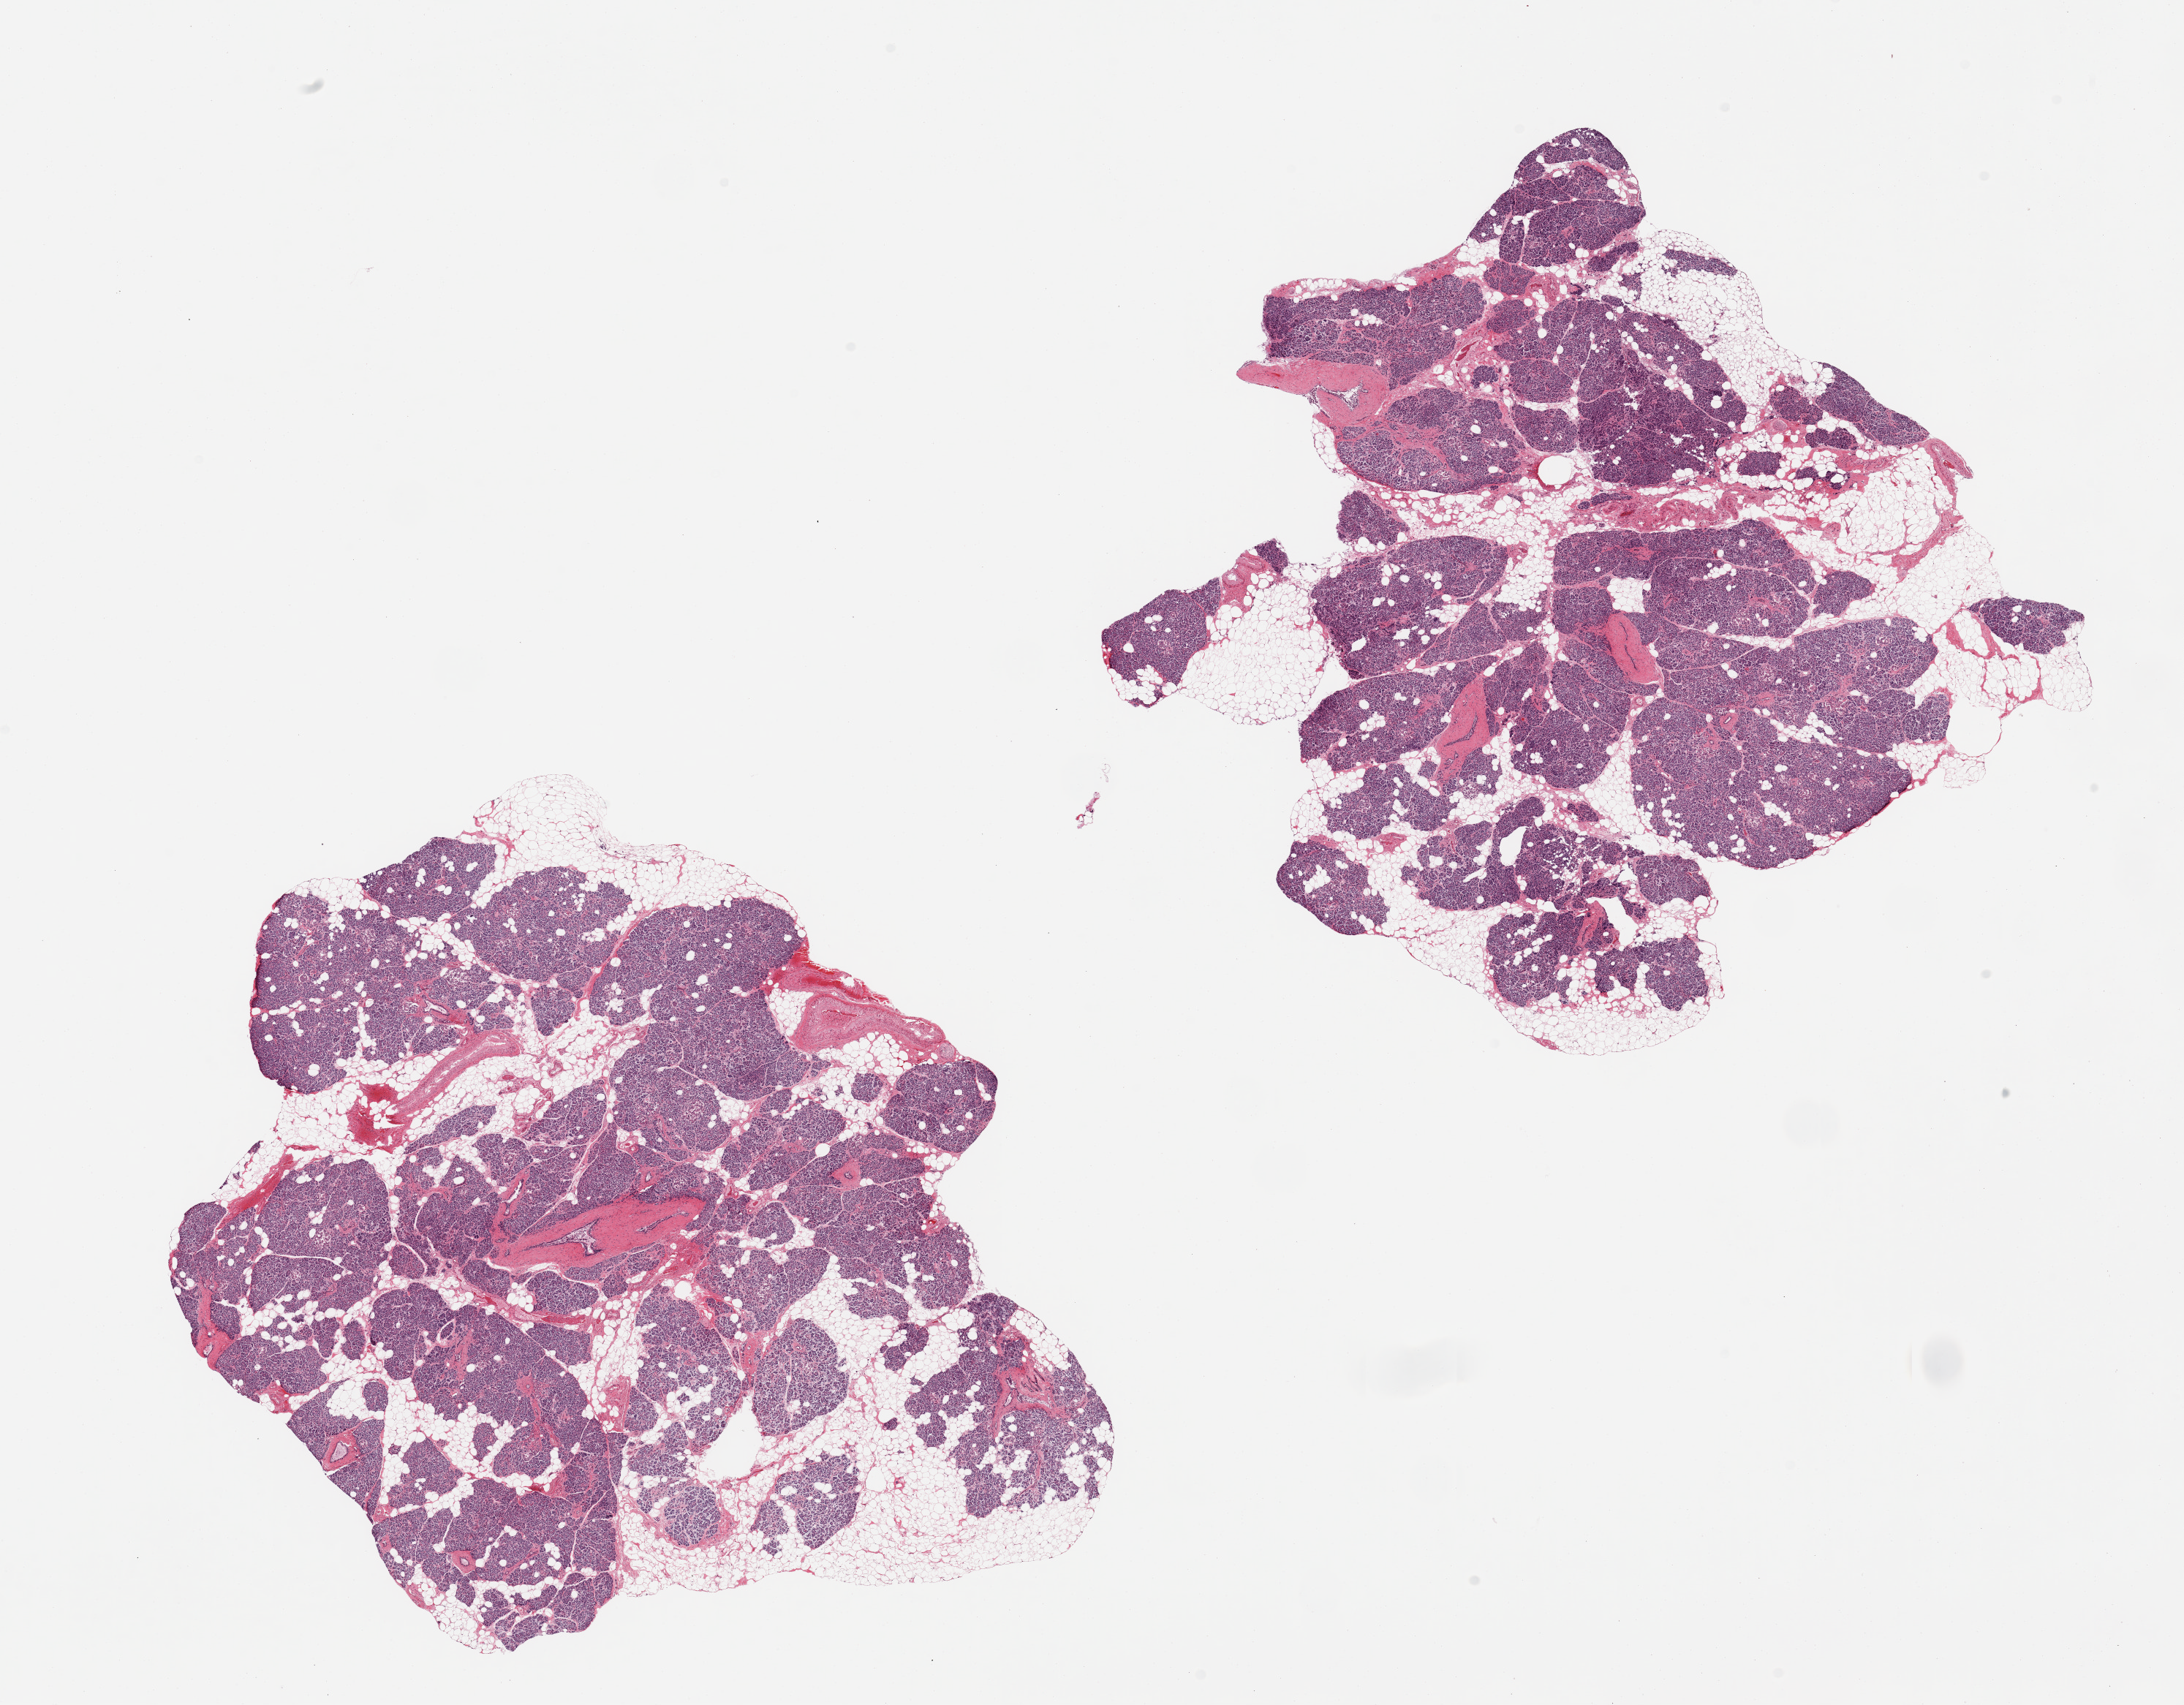
Haematoxylin and eosin whole-slide image, brightfield, a low-resolution overview of the entire scanned area, about 23.6 x 18.4 mm. PAXgene-fixed, paraffin-embedded tissue. Section of pancreas (target tissue). Donor tissue sample. Donor sex: male.
Pathologist's review note for this sample: 2 pieces. 30% internal fat.